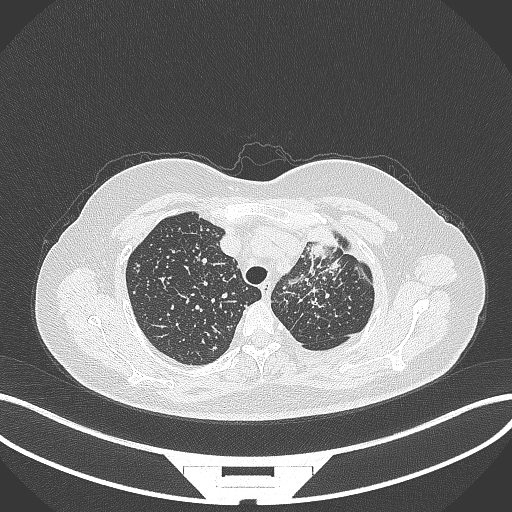
Chest CT, one axial slice; reconstruction kernel B70f; lung window (W 1500 / L -600 HU); 512 × 512 image matrix. Patient: female, 49 years. Case-level facts recorded for this patient, not image findings: clinical TNM (as recorded): T1c N0 M1.
Structures marked on this image (bounding box drawn by a radiologist):
- lung tumour (recorded histology: adenocarcinoma): bounding box [x1, y1, x2, y2] px = [305, 223, 340, 252]